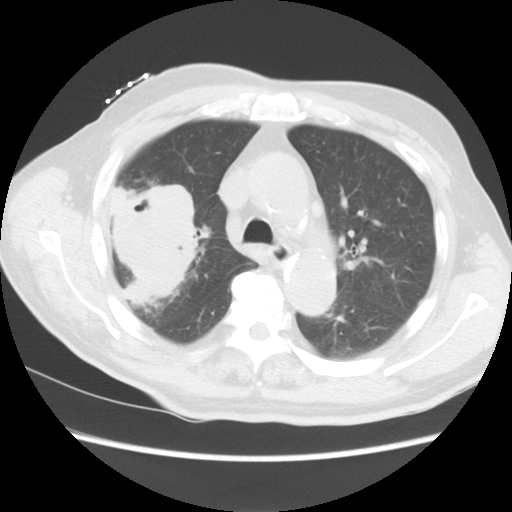
Chest CT, one axial slice. Position 11 of 15 along the scan axis. 120 kVp. Lung window (W 1500 / L -600 HU). 5 mm slice thickness. 512 × 512 image matrix, field of view 350 × 350 mm. Male patient, age 68 years. Case-level facts recorded for this patient, not image findings: clinical TNM (as recorded): T4 N3 M0.
Structures marked on this image (rectangle marked by the reading radiologist):
- lung tumour (recorded histology: squamous cell carcinoma): bounding box (x1, y1, x2, y2) in pixels: (107, 182, 197, 301)